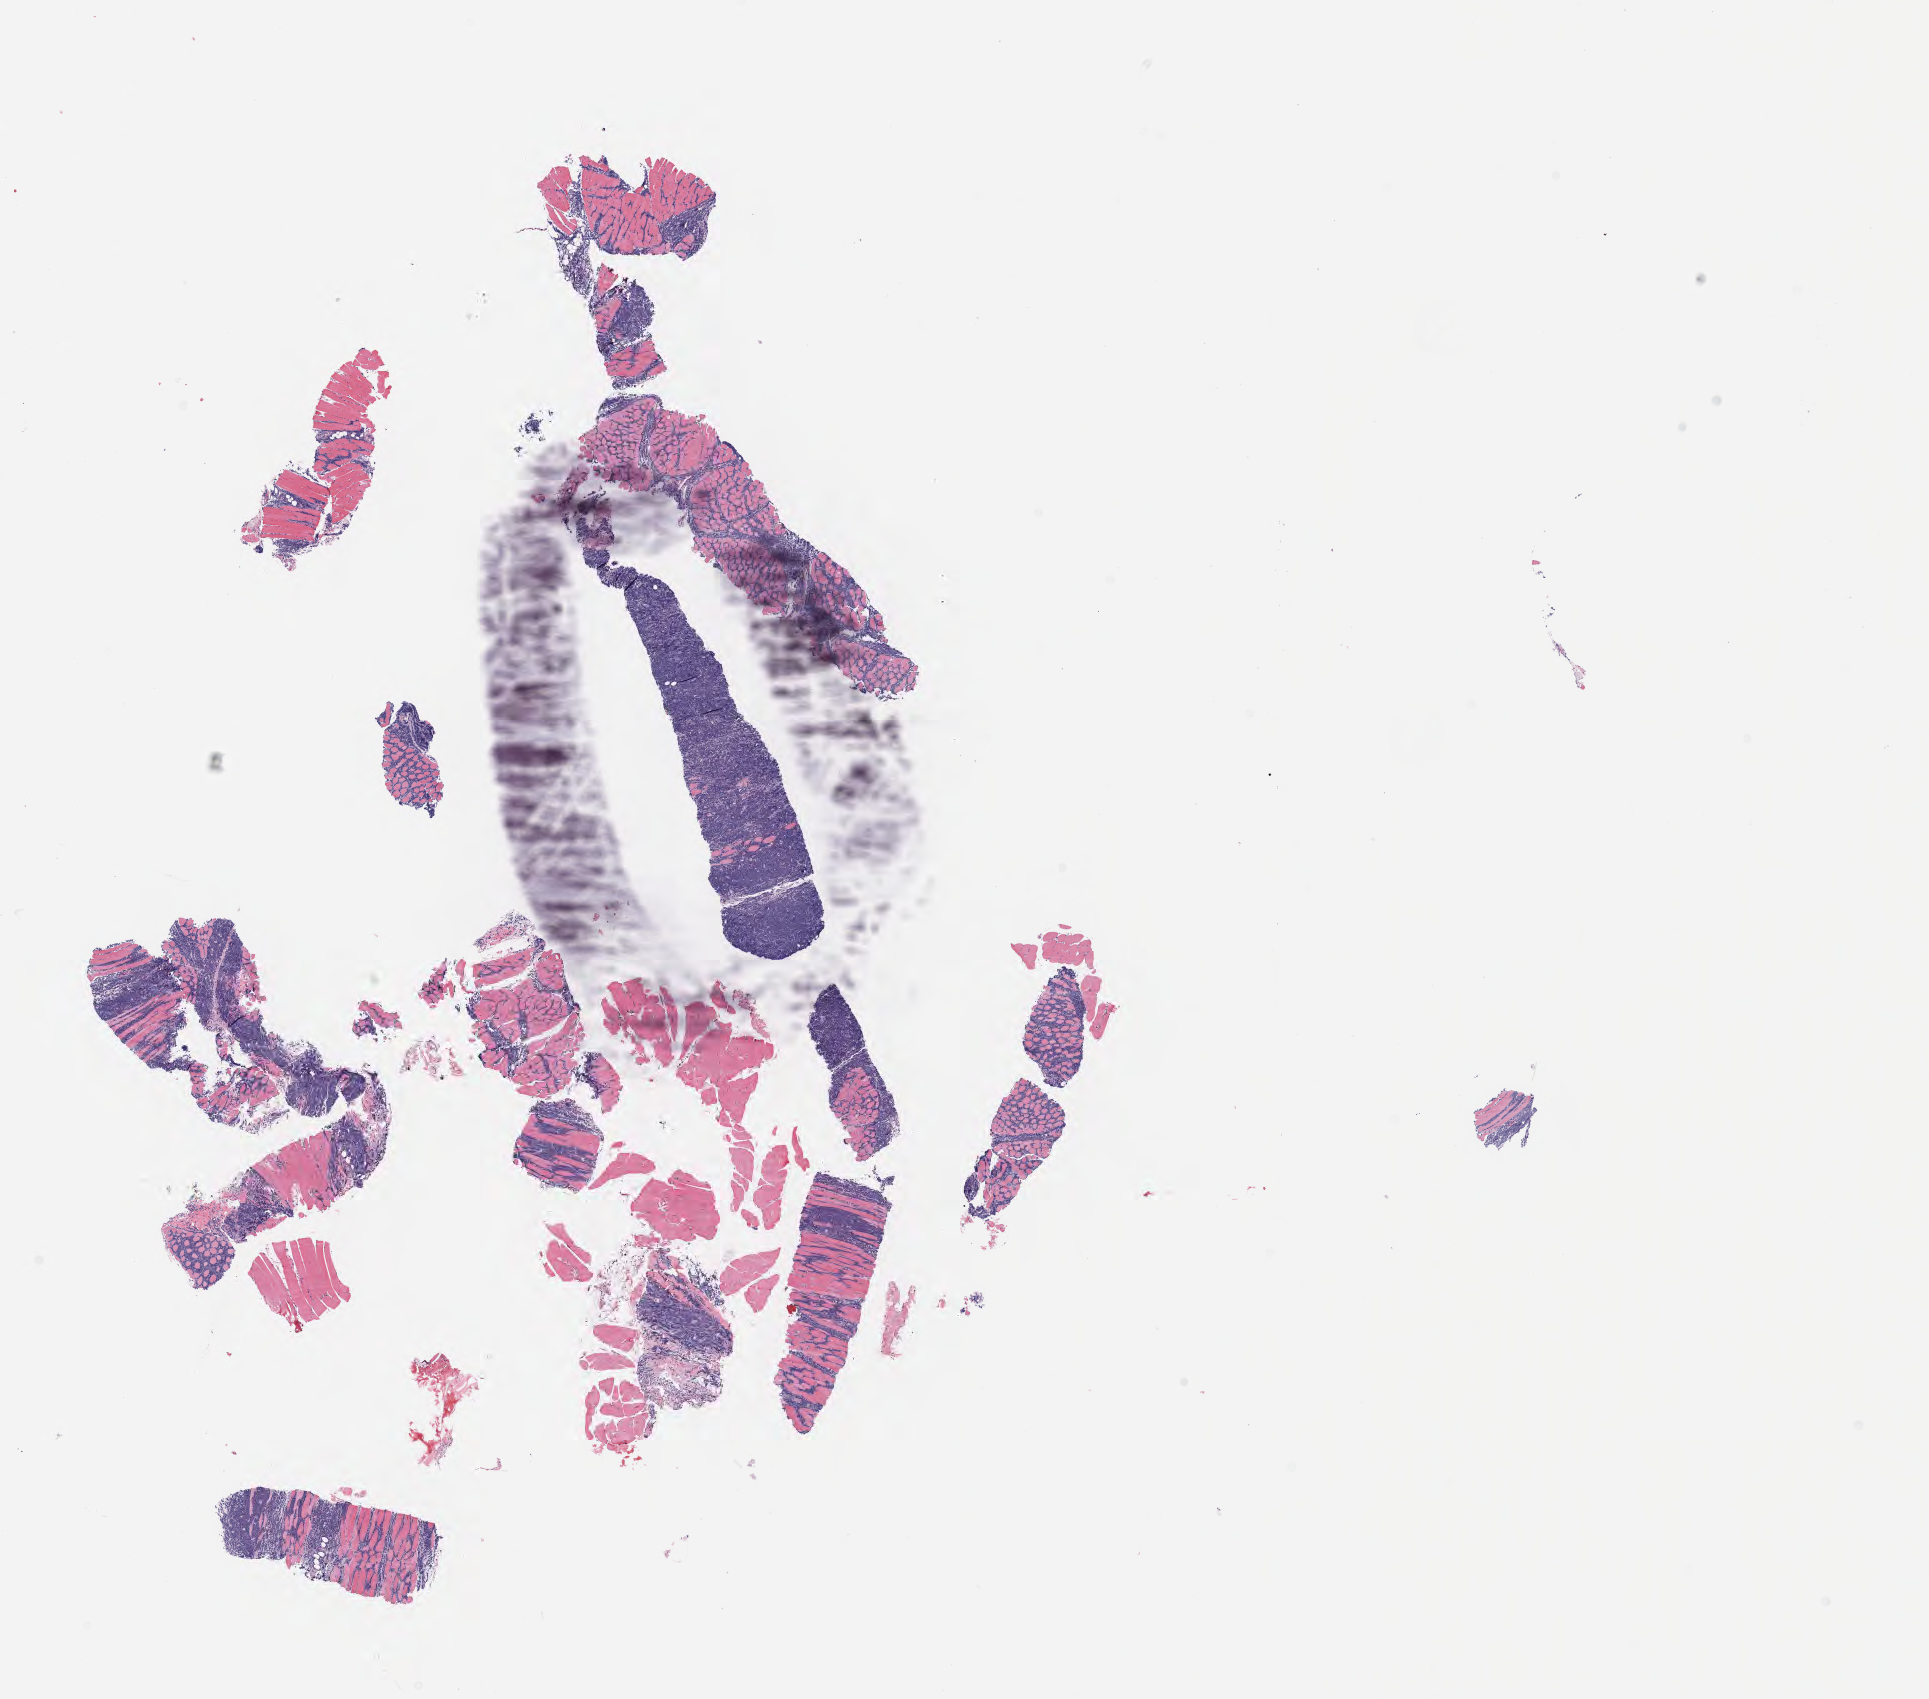
Whole-slide image, haematoxylin and eosin stain — shown as a low-resolution overview of the whole scanned area (about 15.6 x 13.7 mm), tumor tissue, anatomic site: retroperitoneum. Female patient, aged 53.
Histologic diagnosis: Burkitt lymphoma, NOS.